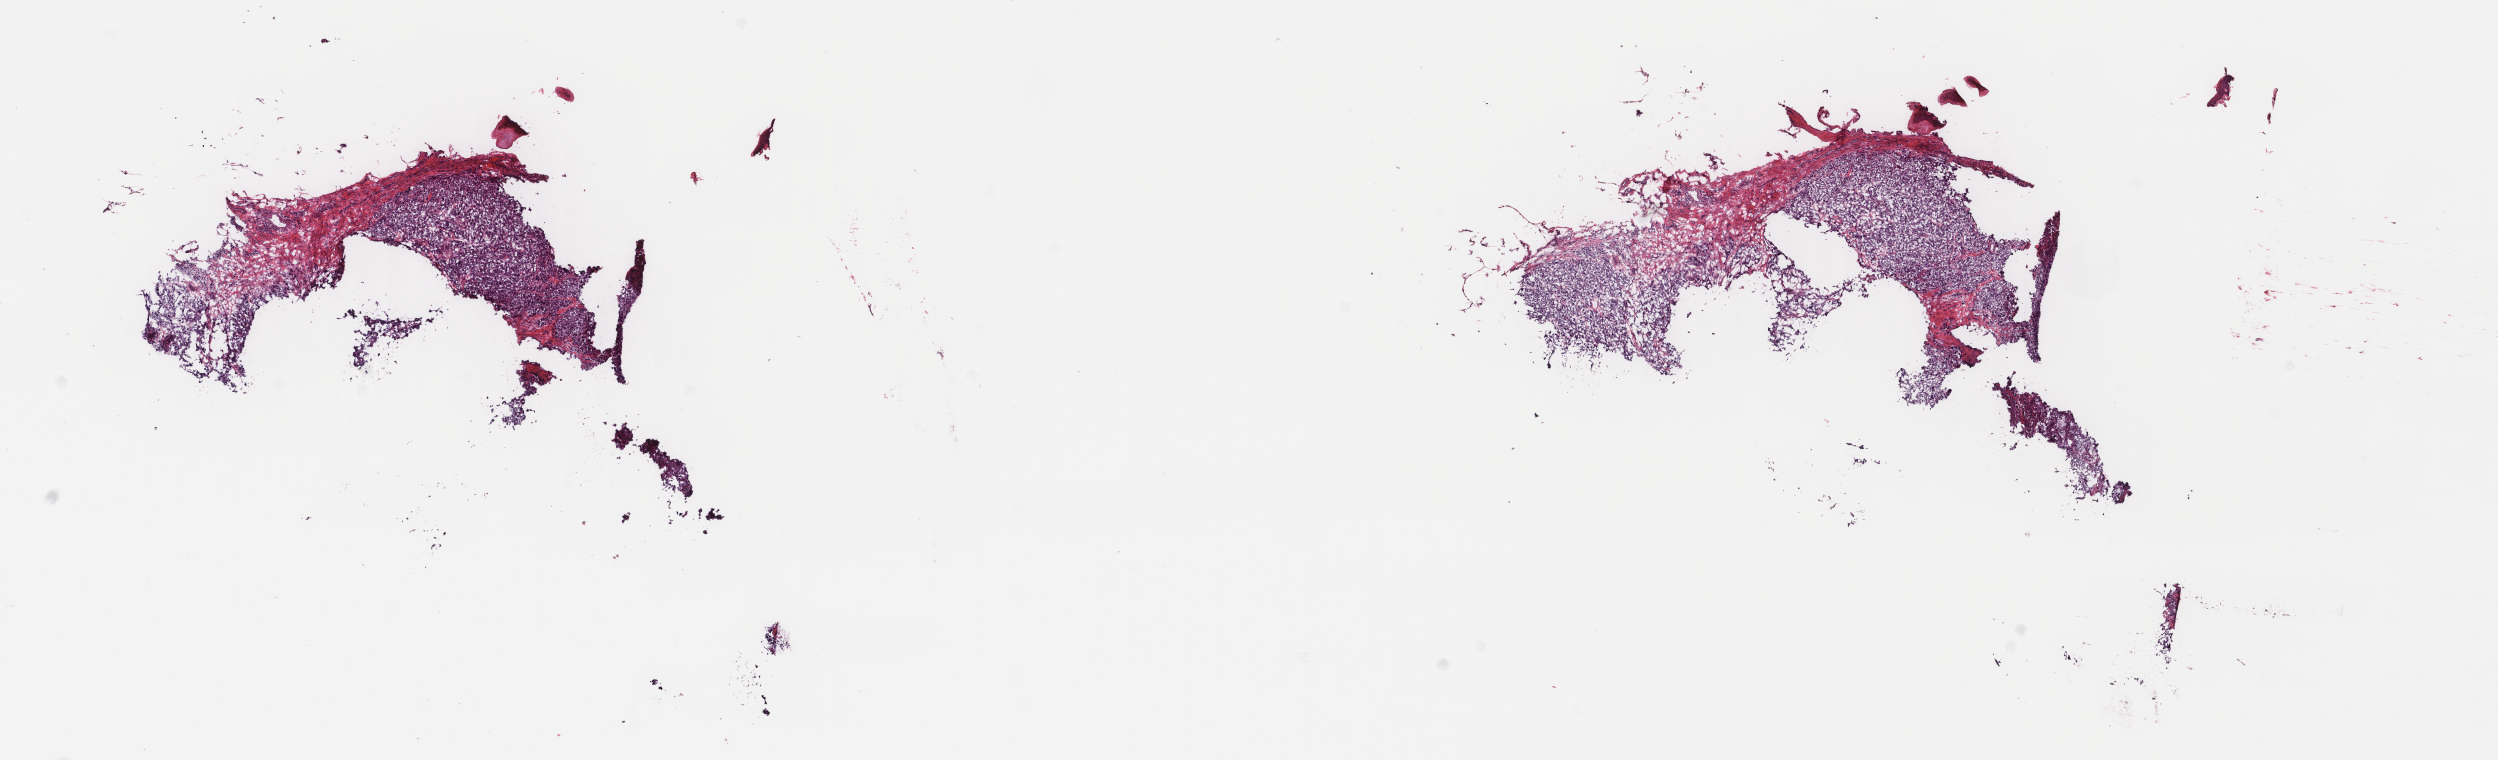
H&E whole-slide image, a low-resolution overview of the entire scanned area, about 19.8 x 6.0 mm (from a 40x scan). Frozen section. Metastatic tumour sample, sampled site: connective, subcutaneous and other soft tissues. Female patient; age at initial diagnosis 69 years. Composition of this section per pathologist review: tumour cells 90%, tumour nuclei 90%, normal cells 0%, stromal cells 10%, necrosis 0%. Infiltration values recorded for this section: lymphocyte infiltration 1%, monocyte infiltration 0%, neutrophil infiltration 0%.
- this section: metastatic tumour tissue
- patient diagnosis: Malignant melanoma, NOS